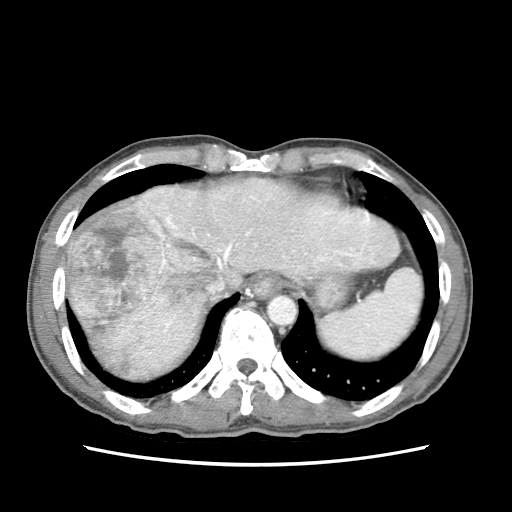
Contrast-enhanced abdominal CT (liver protocol), one axial slice; position 62 of 79 along the scan axis; soft-tissue window (W 400 / L 40 HU); 2.5 mm slice thickness; 512 × 512 image matrix. From the clinical record (not read from this slice): diagnosis: hepatocellular carcinoma (patient treated with transarterial chemoembolisation; whether this scan precedes or follows treatment is not stated here); TNM stage (as recorded): Stage-IIIB; Child-Pugh class: A; tumour differentiation: moderately differentiated; tumour nodularity: multinodular.
Annotated regions visible in this slice (semi-automatic segmentation, software-assisted and operator-edited):
- abdominal aorta: bounding box <268,297,296,325> (left, top, right, bottom; pixels)
- liver parenchyma outside the tumour (the mass and vessels are separate outlines, so this box may not span the whole liver): <66,178,400,380>
- mass: <67,195,216,375>
- liver vessels: <152,186,353,342>